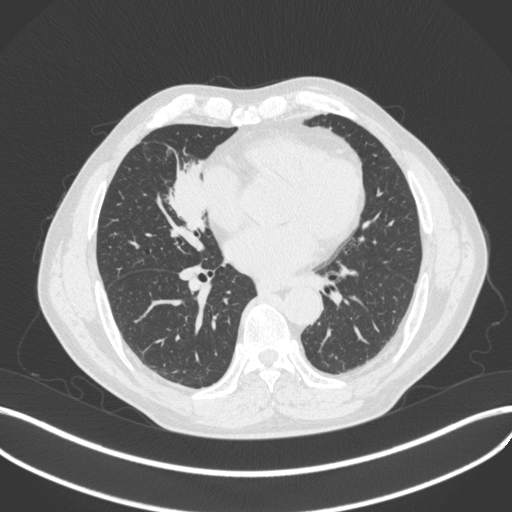
Chest CT, one axial slice; slice 176 of 429 in the series (ordered by position); reconstruction kernel B31f; 120 kVp; lung window (W 1500 / L -600 HU); 1 mm slice thickness; 512 × 512 image matrix, field of view 400 × 400 mm. Male patient, age 61 years. Case-level facts recorded for this patient, not image findings: clinical TNM (as recorded): T2b N1 M0.
Annotated regions visible in this slice (bounding box drawn by a radiologist):
- lung tumour (recorded histology: squamous cell carcinoma): bounding box (x1, y1, x2, y2) in pixels: (164, 151, 209, 233)